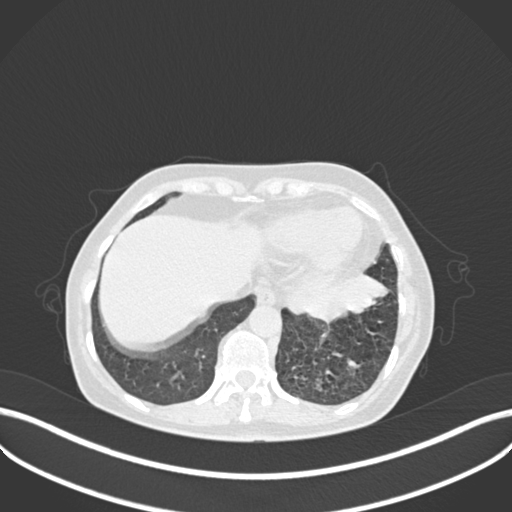
Chest CT, one axial slice; slice 54 of 270 in the series (ordered by position); lung window (W 1500 / L -600 HU); 1 mm slice thickness; 512 × 512 image matrix, field of view 400 × 400 mm. Female patient, age 63 years. Case-level facts recorded for this patient, not image findings: clinical TNM (as recorded): T1b N0 M0.
Structures marked on this image (bounding box drawn by a radiologist):
- lung tumour (recorded histology: adenocarcinoma): box from (x=282, y=266) to (x=386, y=324) px